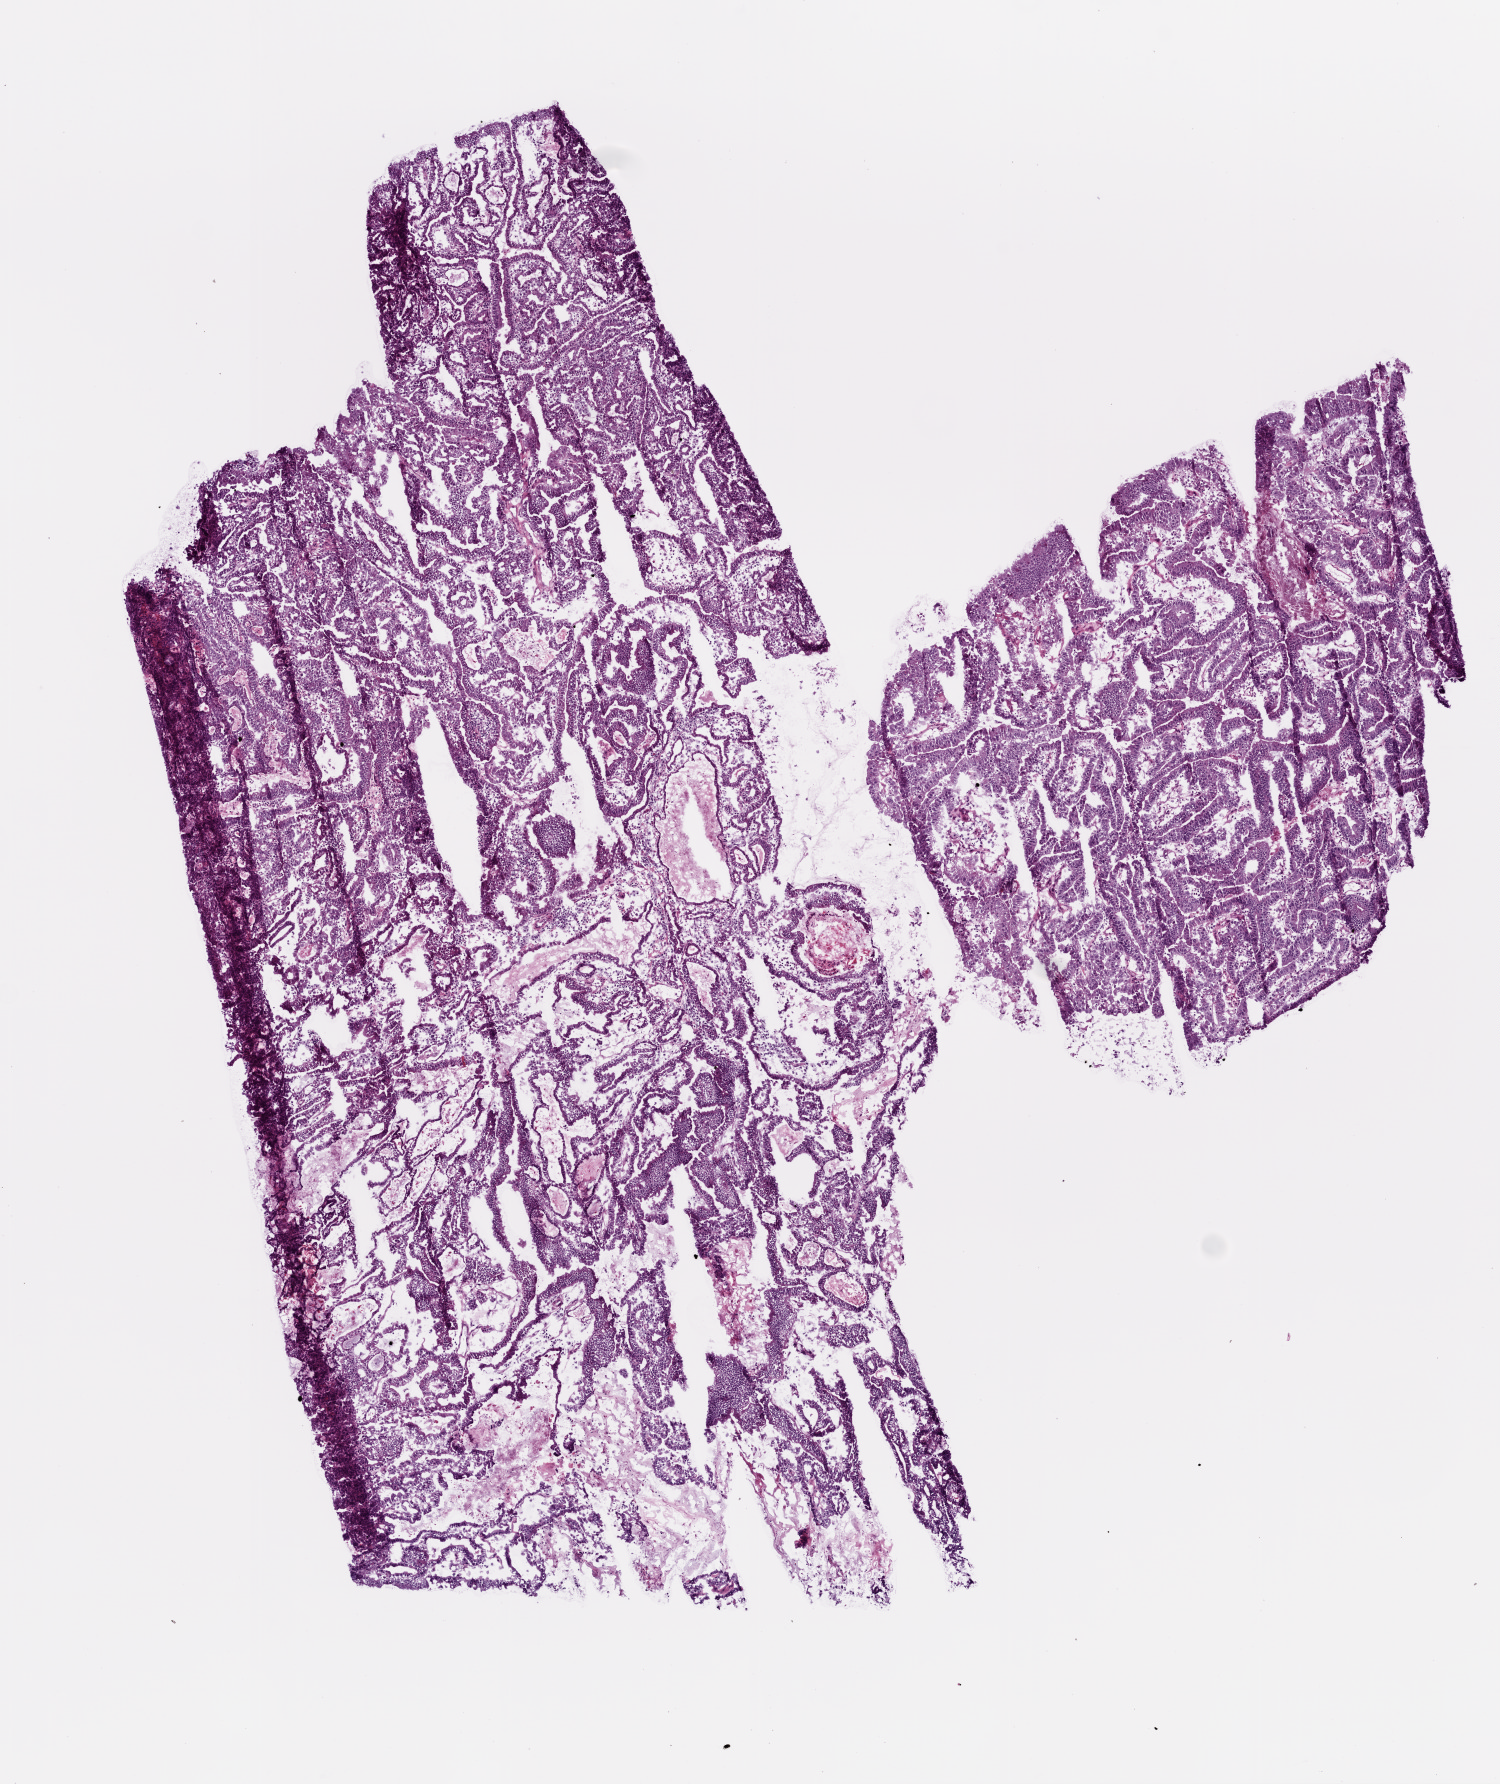
Whole-slide histology image, Hematoxylin and eosin (H&E) stained — low-resolution overview of the scanned area, about 6.0 x 7.2 mm (slide scanned at 20x), frozen section, primary tumour sample from the stomach. Patient: male, age at initial diagnosis 66 years. Histologic grade: G2 (moderately differentiated). Composition of this section per pathologist review: tumour cells 87%, tumour nuclei 75%, normal cells 0%, stromal cells 10%, necrosis 3%.
• TNM: T2 N3 M0
• pathologic diagnosis: Adenocarcinoma, intestinal type (cardia, NOS)
• AJCC pathologic stage: IV